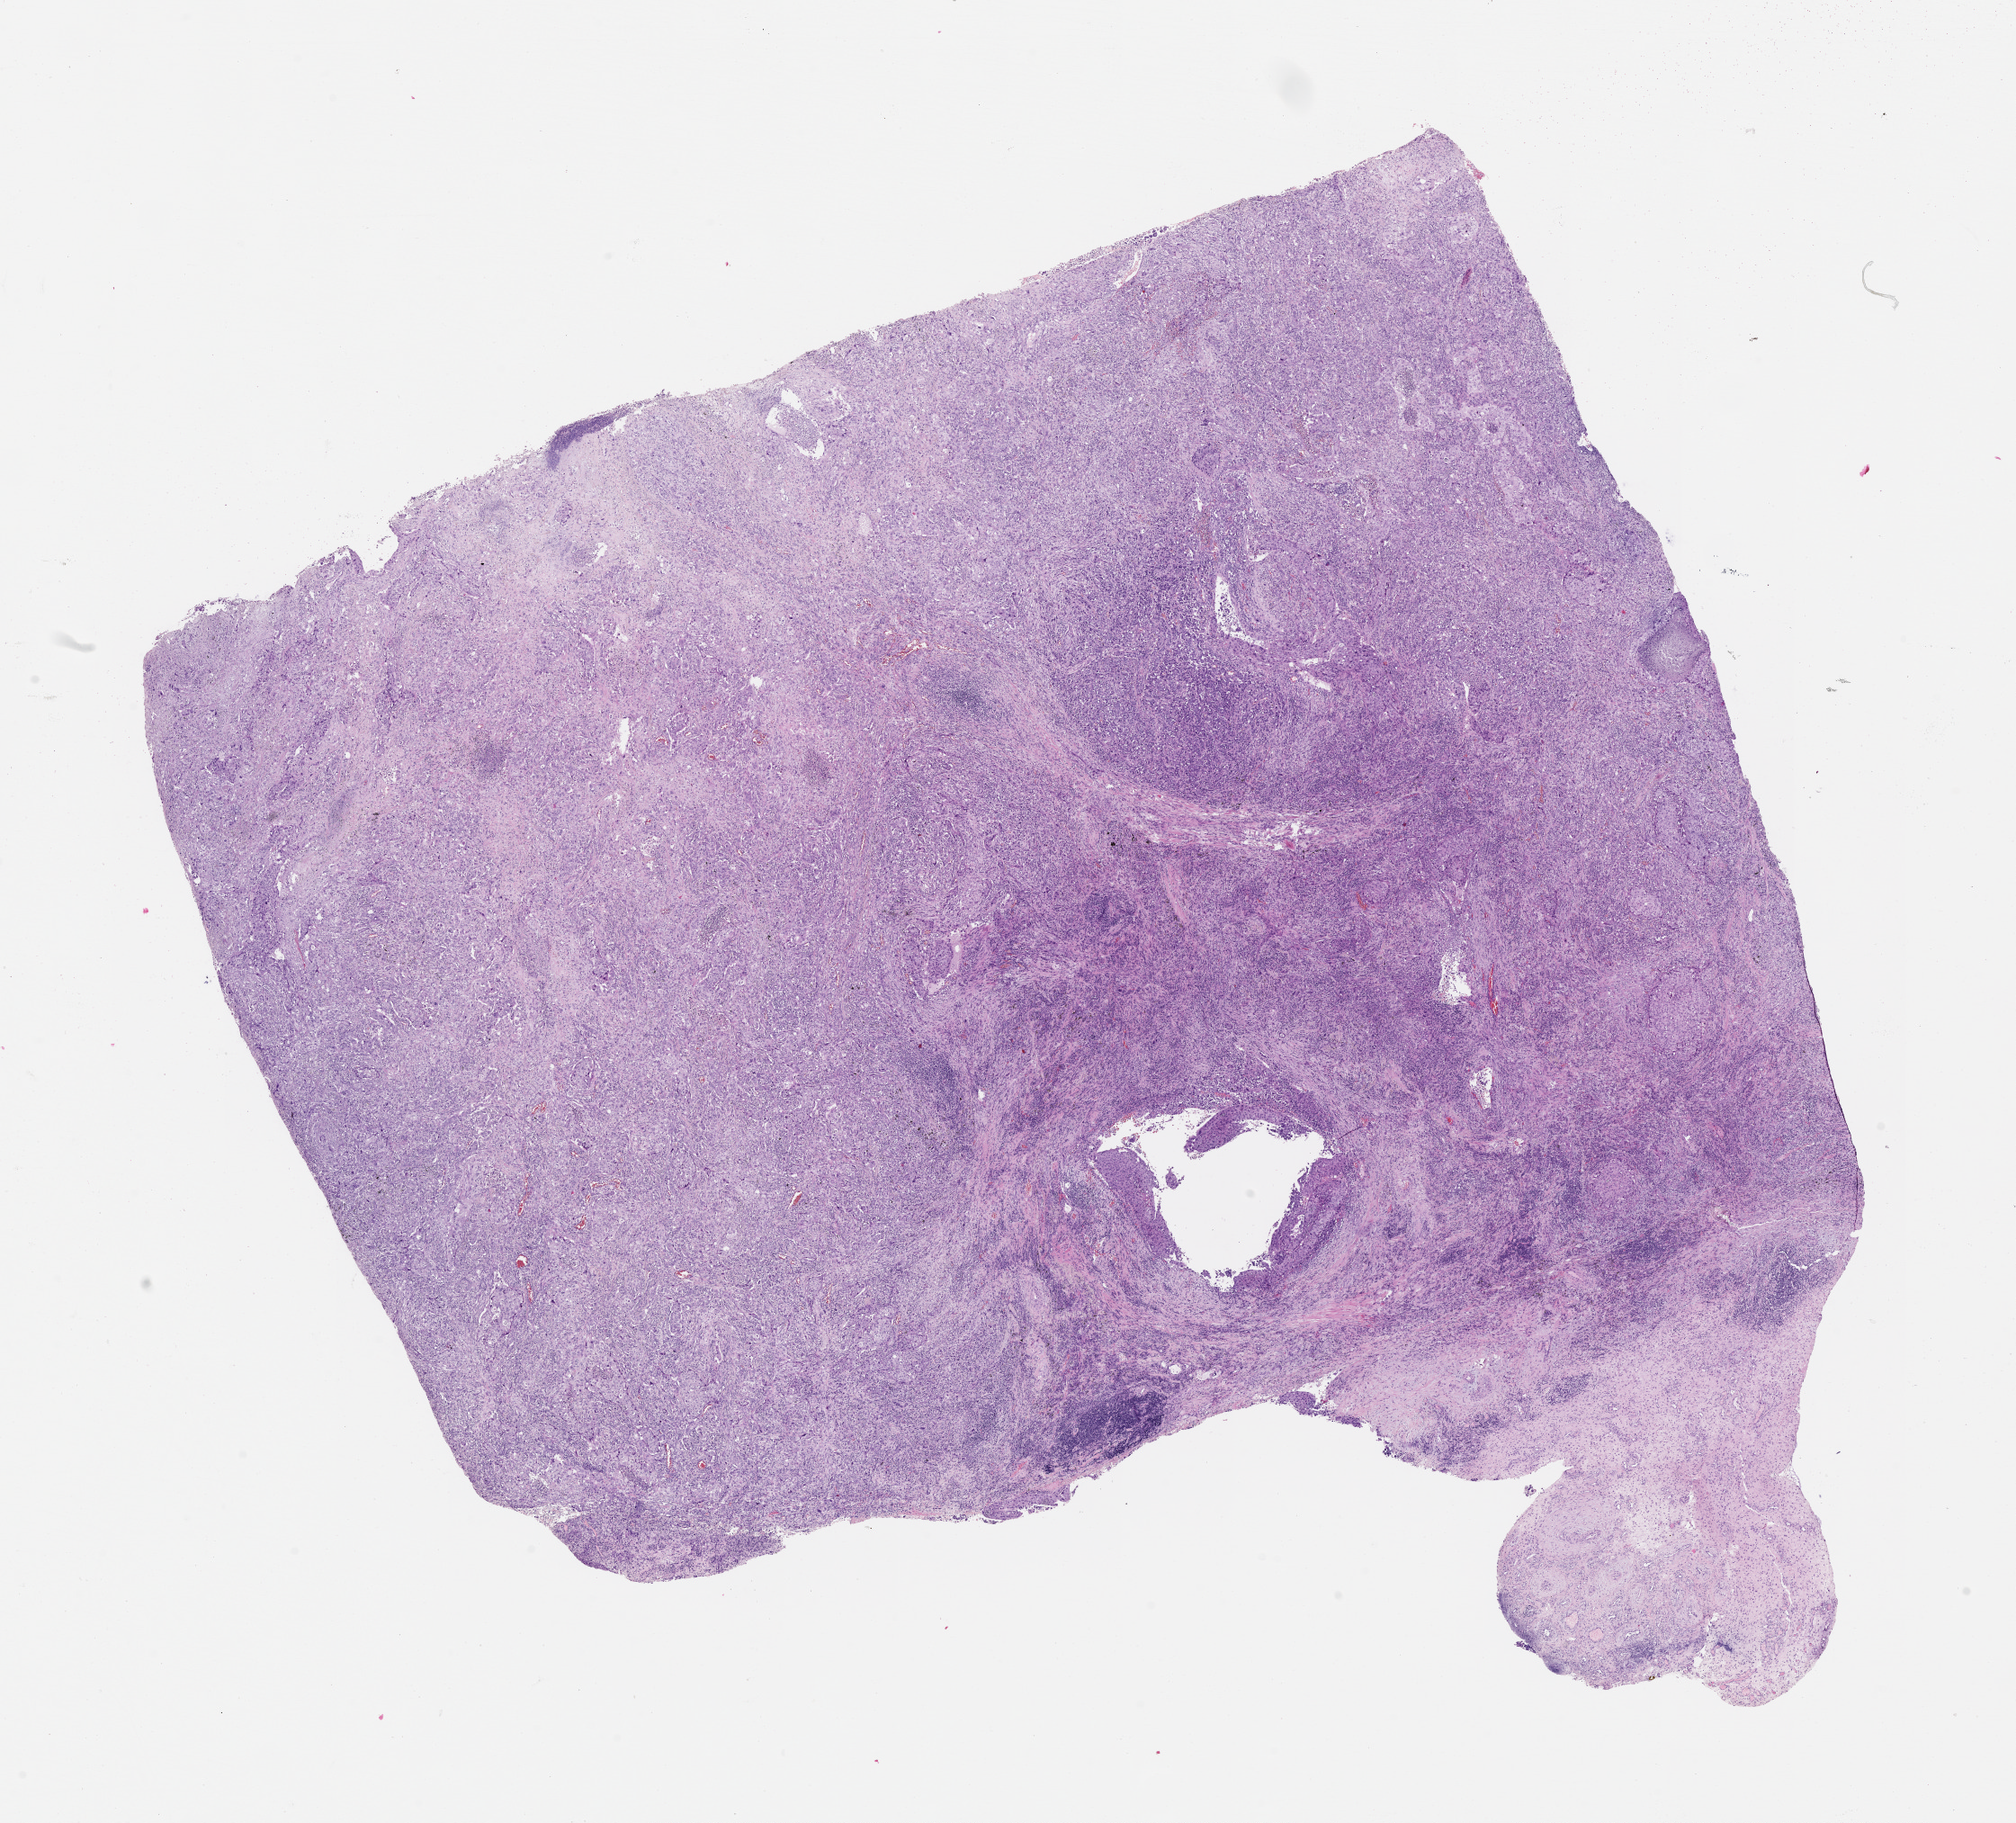
Whole-slide histology image, H&E-stained — shown as a low-resolution overview of the whole scanned area (about 18.0 x 16.3 mm, acquisition: 20x scan). Lung, tissue type not recorded.
• patient diagnosis (cohort enrolment): squamous cell carcinoma (lung)